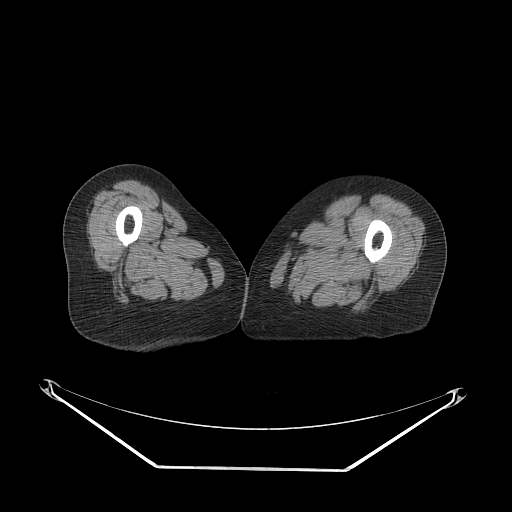
CT of an extremity soft-tissue mass (from a PET/CT study), one axial slice. Position 57 of 91 along the scan axis. Soft-tissue window (W 400 / L 40 HU). 3.75 mm slice thickness. 512 × 512 image matrix, field of view 500 × 500 mm. Female patient. From the clinical record (not read from this slice): histological type: pleomorphic leiomyosarcoma; grade: high; site of the primary tumour: left thigh.
Structures marked on this image (expert contour drawn on MRI and transferred to this co-registered scan by the dataset authors):
- gross tumour volume including surrounding oedema: bounding box (x1, y1, x2, y2) in pixels: (279, 208, 300, 225)